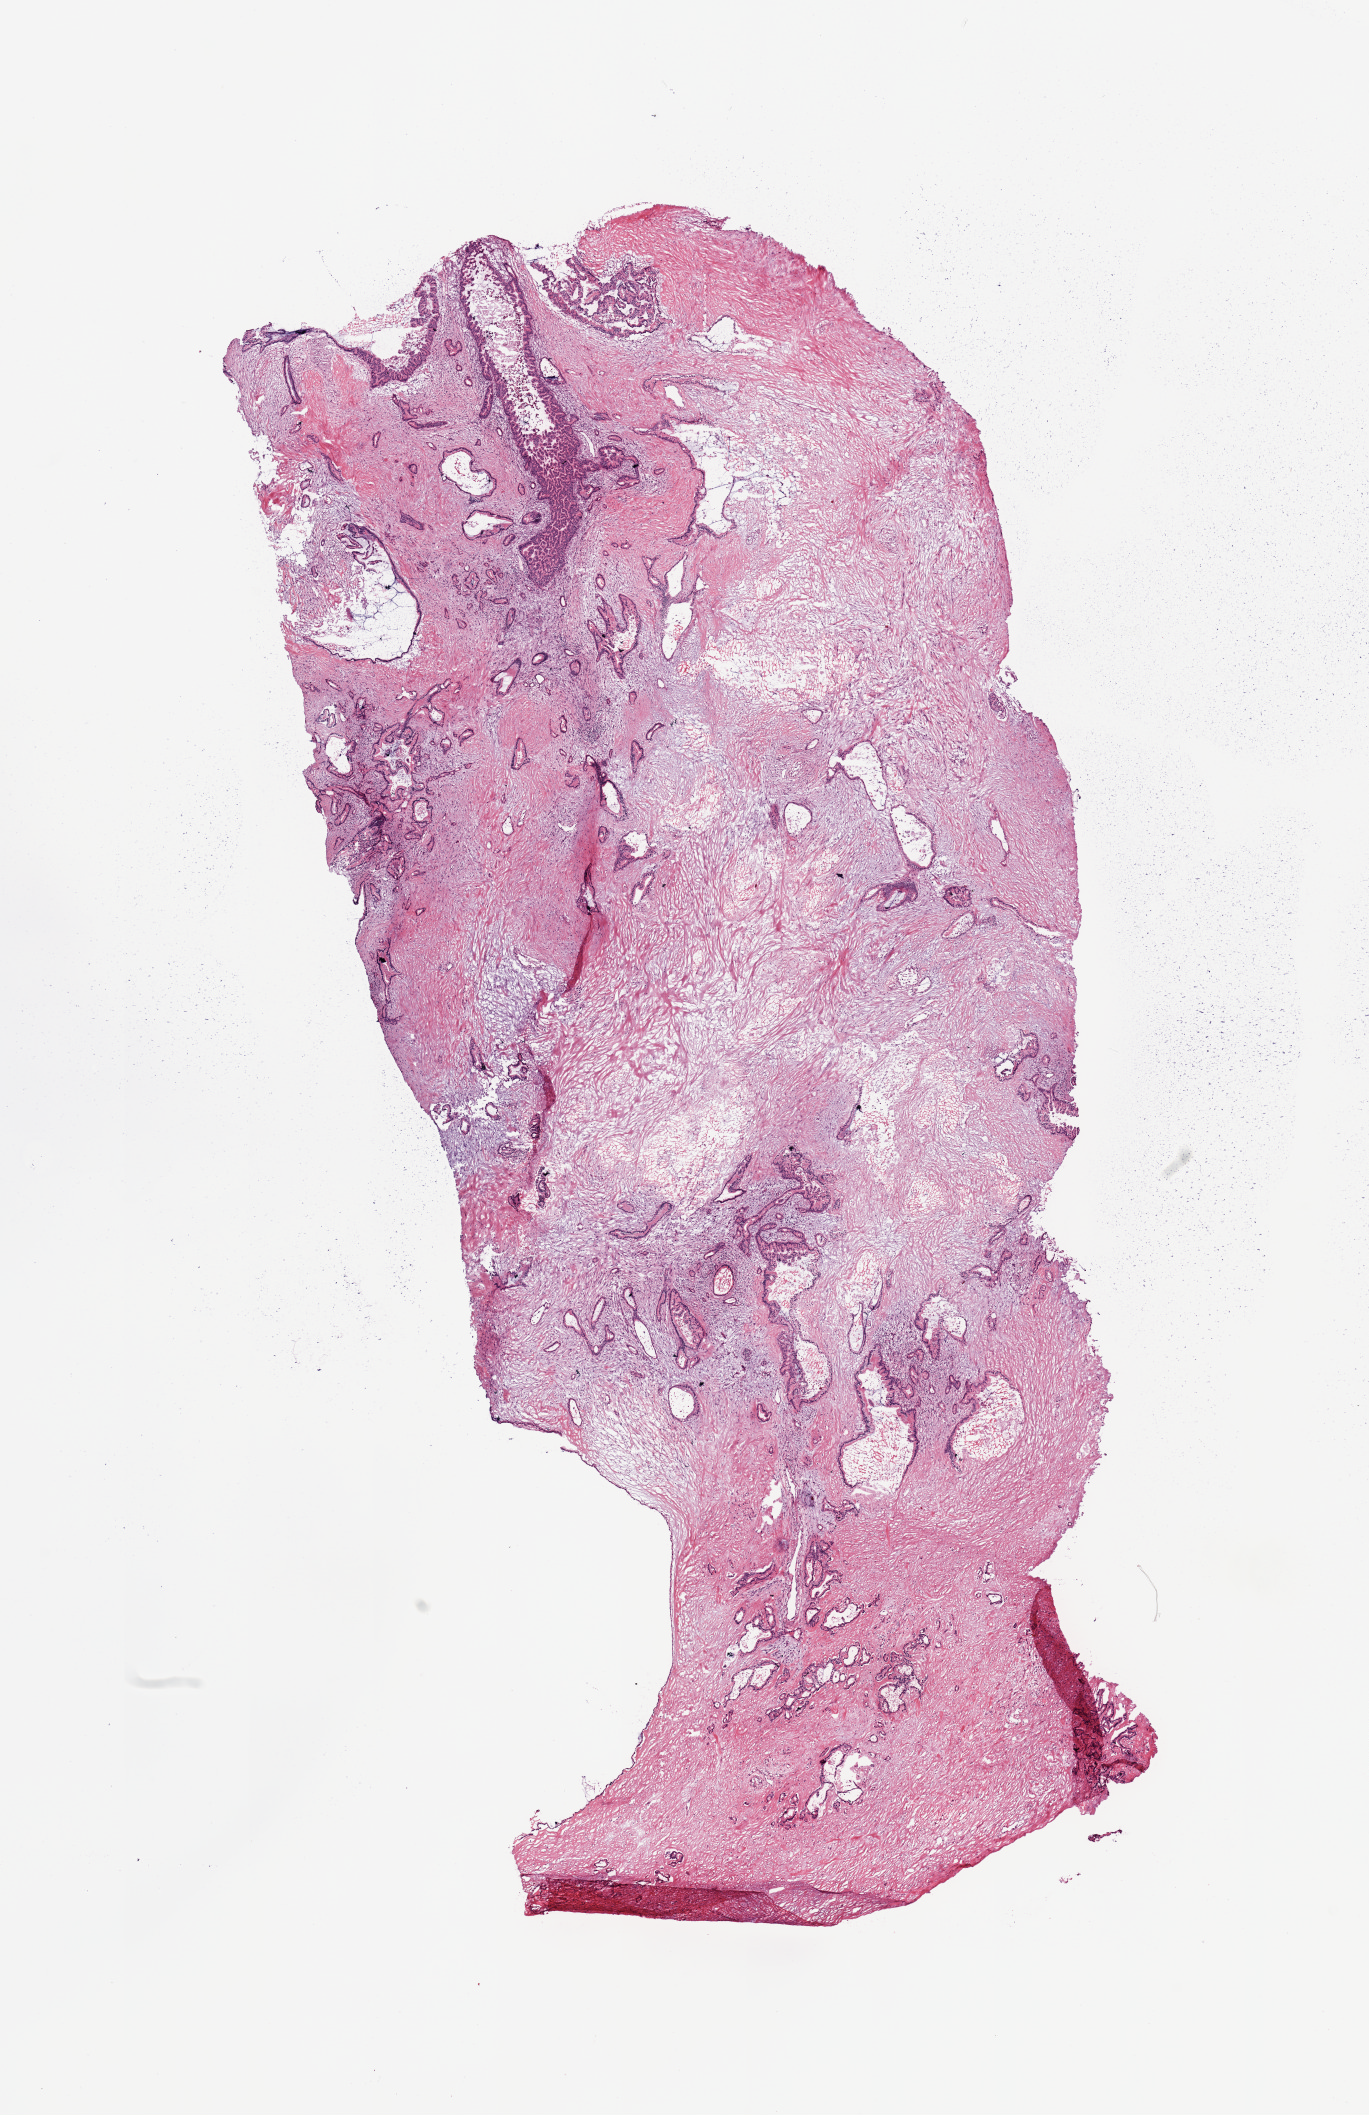
Digitized H&E-stained tissue section (whole slide) — shown as a low-resolution overview of the whole scanned area (about 10.8 x 16.7 mm, slide scanned at 20x). Tumour tissue sample, sampled site: pancreas. Male, 69 y/o. Histologic grade: G2 (moderately differentiated). Slide review estimates, as recorded: tumour nuclei 70%, necrosis 0%.
* diagnosis: Infiltrating duct carcinoma, NOS
* primary tumour site (as recorded): tail
* AJCC pathologic stage: IIB